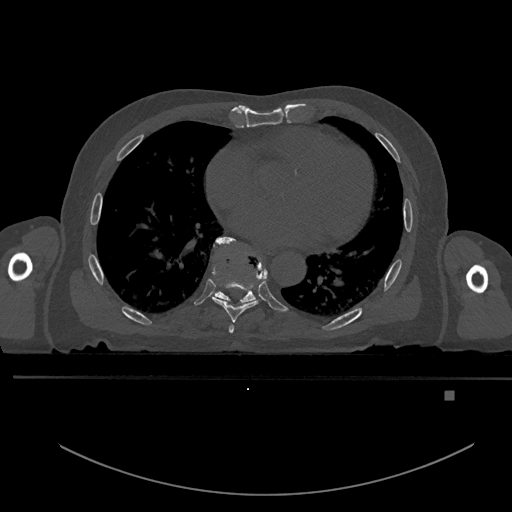
CT including the spine, one axial slice. Position 235 of 969 along the scan axis. Bone window (W 1800 / L 400 HU). 0.5 mm slice thickness. 512 × 512 image matrix, field of view 456 × 456 mm. Male patient, age 82 years. Case-level facts recorded for this patient, not image findings: primary cancer: prostate; vertebrae with lytic lesions (as recorded): T11, T9, T8, T2.
Structures marked on this image (semi-automatically segmented with operator editing):
- T6 vertebra: bounding box [x1, y1, x2, y2] px = [228, 324, 234, 333]
- T7 vertebra: [212, 236, 268, 322]
- T8 vertebra: [212, 239, 261, 306]